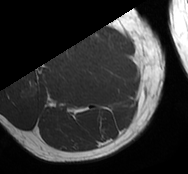
MRI of an extremity soft-tissue mass, one axial slice. Slice 16 of 93 in the series (ordered by position). MR volume resampled by the dataset authors to the PET/CT grid (not the native acquisition matrix). 3.27 mm slice thickness. 188 × 174 image matrix, field of view 184 × 170 mm. Male patient. From the clinical record (not read from this slice): histological type: undifferentiated - pleiomorphic; grade: high; site of the primary tumour: right thigh.
Annotated regions visible in this slice (expert contour drawn on MRI and transferred to this co-registered scan by the dataset authors):
- gross tumour volume including surrounding oedema: bounding box [x1, y1, x2, y2] px = [63, 49, 76, 63]